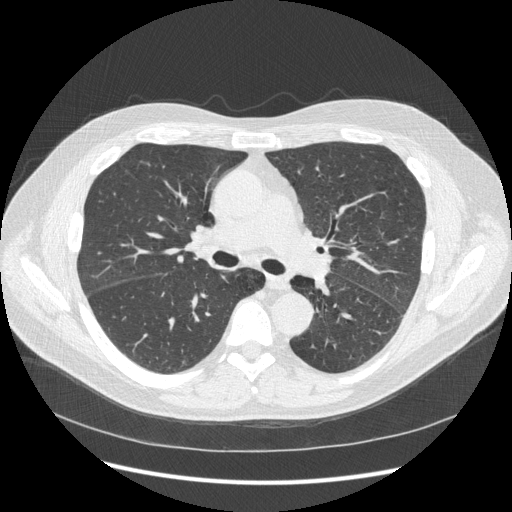
Axial slice from a low-dose chest CT screening exam. Second screening round (one year after baseline). Lung window (W 1500 / L -600 HU). 1.25 mm slice thickness. Male participant, aged 59 years at enrolment. Current smoker at enrolment.
• Expert-annotated lung lesion, box from (x=185, y=218) to (x=237, y=256) px.
• Reader record for this screening exam (exam-level; its link to the box is not recorded): non-calcified nodule or mass ≥4 mm, lingula, 5 × 5 mm, smooth margins, soft tissue attenuation, pre-existing on the prior screen: yes; interval growth: no.
• Note: the box lies in the patient's right hemithorax on this image, whereas the reader's record names the left lung; they may be different findings.
• Participant outcome: lung cancer diagnosed 540 days after this screen — squamous cell carcinoma, keratinizing, NOS, right hilum, stage IIIB (AJCC 6th edition).